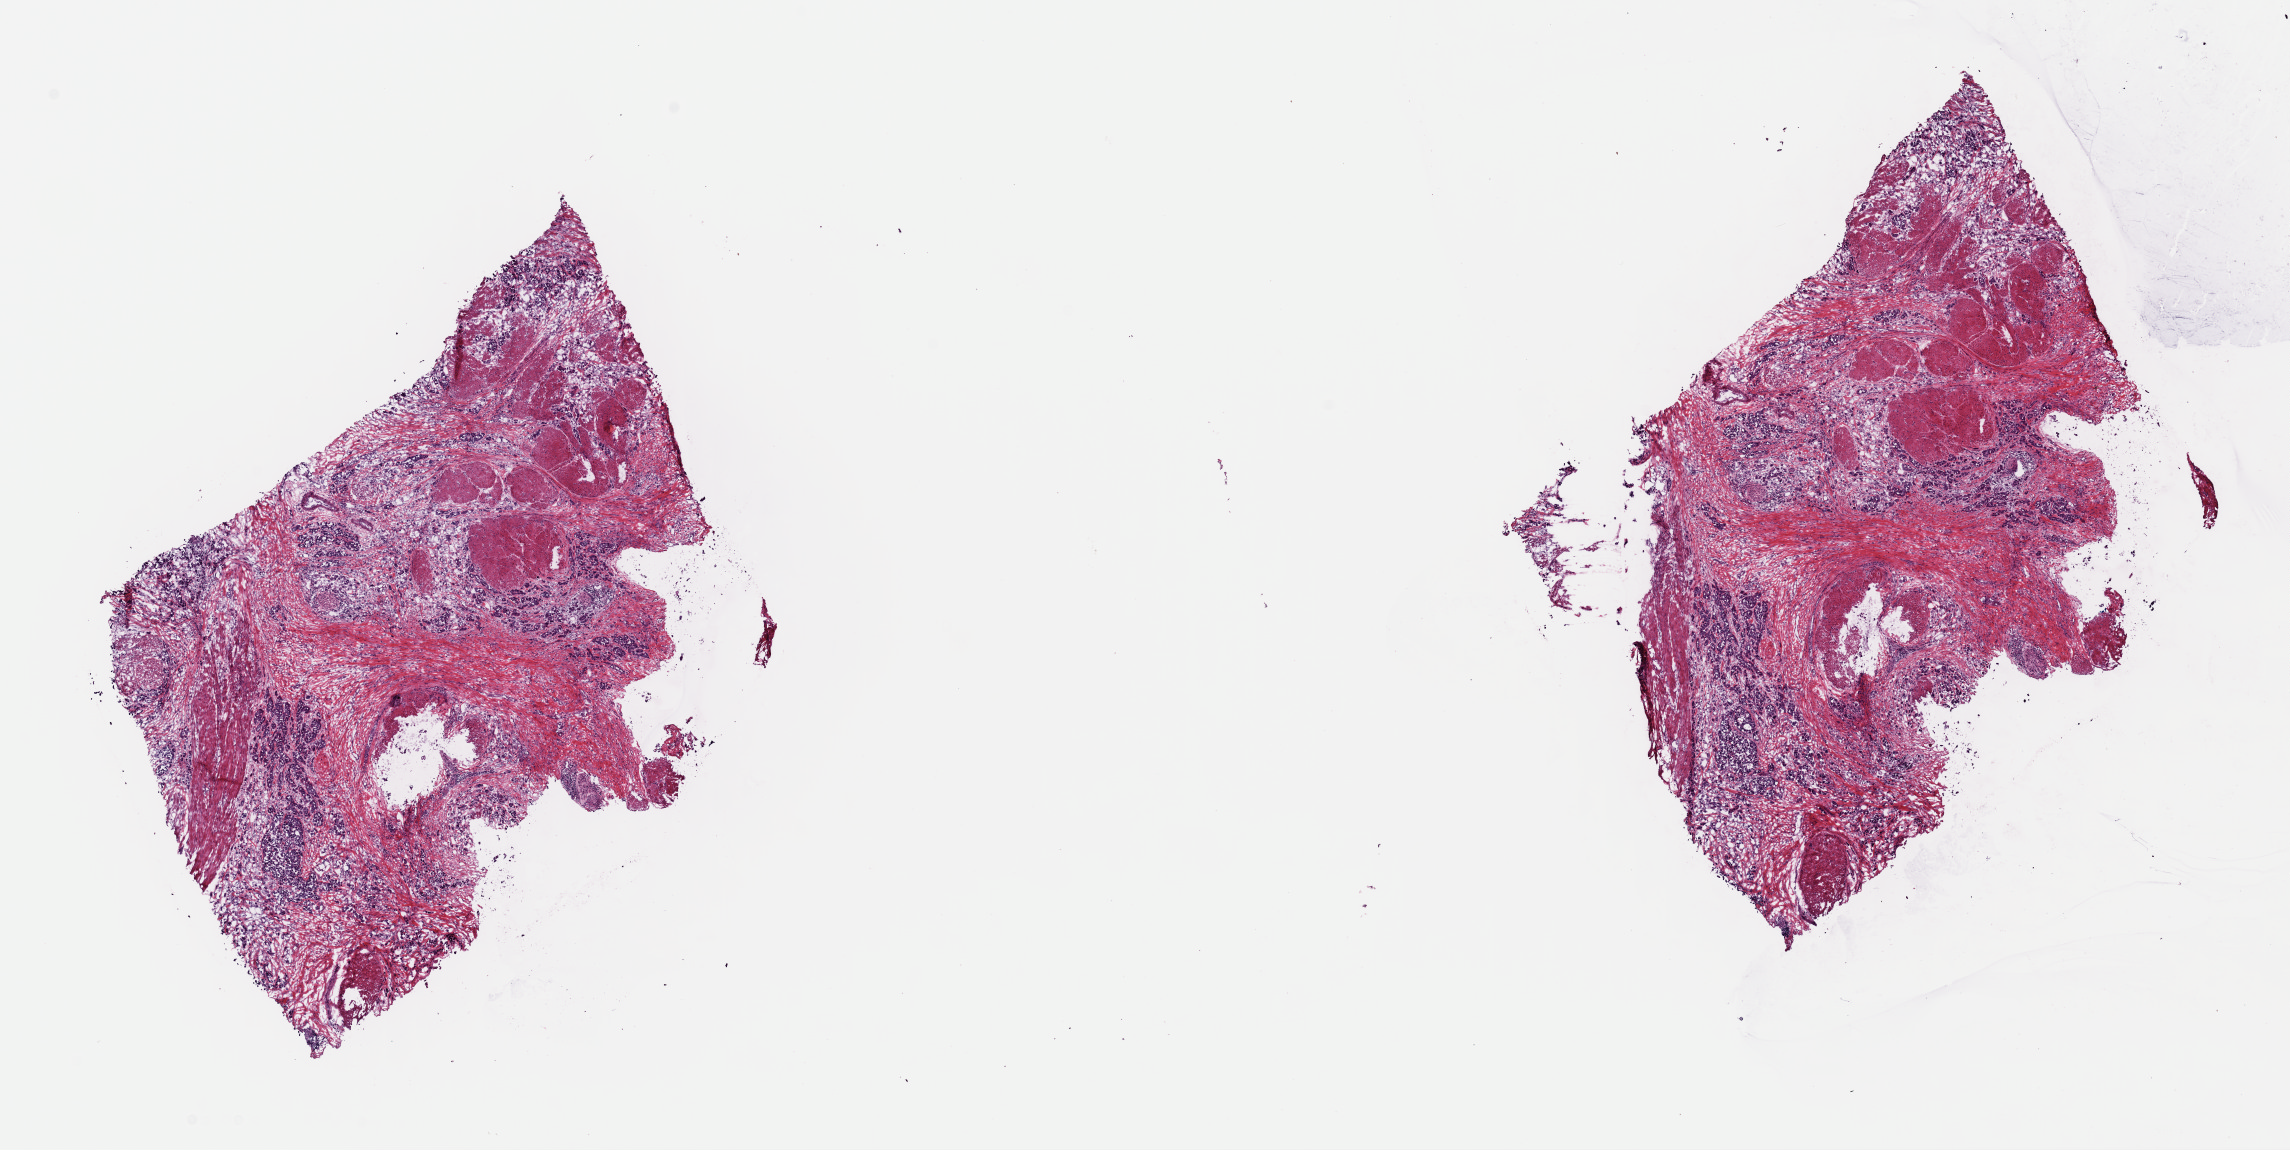
H&E whole-slide image — shown as a low-resolution overview of the whole scanned area (about 18.1 x 9.1 mm, acquisition: 40x scan). Frozen section. Primary tumour sample from the bladder. Female patient; age at initial diagnosis 80 years. Histologic grade: high grade. Slide review estimates, as recorded: tumour cells 70%, tumour nuclei 70%, normal cells 0%, stromal cells 30%, necrosis 0%. Inflammatory infiltration, as recorded: lymphocyte infiltration 3%, monocyte infiltration 0%, neutrophil infiltration 0%.
• AJCC pathologic stage: IV
• diagnosis: Transitional cell carcinoma
• TNM: T3 N2 M0
• lymph nodes positive (case pathology): 4 of 35 examined